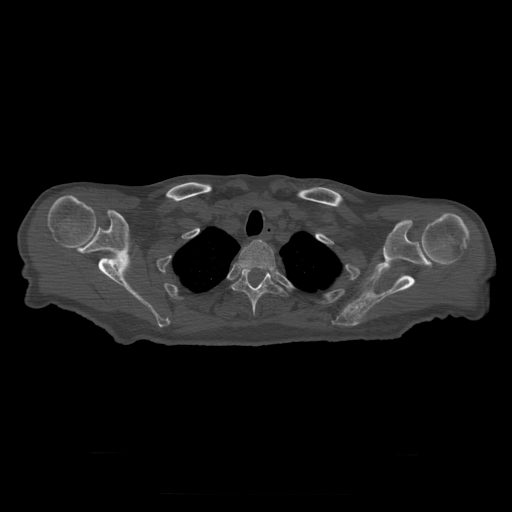
CT including the spine, one axial slice; slice 263 of 397 in the series (ordered by position); reconstruction kernel STANDARD; bone window (W 1800 / L 400 HU); 1.25 mm slice thickness; 512 × 512 image matrix. Patient age 73 years. Case-level facts recorded for this patient, not image findings: primary cancer: prostate.
Outlined on this slice (semi-automatic segmentation, software-assisted and operator-edited):
- T2 vertebra: box from (x=238, y=240) to (x=276, y=271) px
- T3 vertebra: (x=232, y=268)–(x=286, y=316)